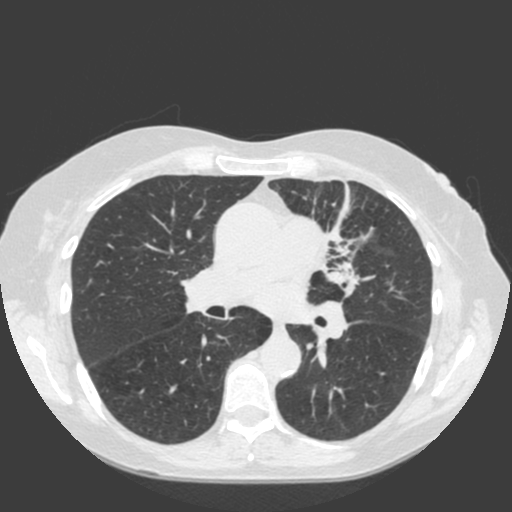
Low-dose screening chest CT, axial slice; baseline annual screen; lung window (W 1500 / L -600 HU); standard (soft-tissue) reconstruction kernel (C); slice 77 of 184 in the series. Female, age 66 years at enrolment. Current smoker at enrolment.
Expert reader's lesion annotation, bounding box [x1, y1, x2, y2] px = [275, 196, 403, 312]. The exam's reader record, not a measurement of the box and not confirmed to be the same lesion: non-calcified nodule or mass ≥4 mm, left upper lobe, 61 × 45 mm, spiculated (stellate) margins, soft tissue attenuation. Official screen result: positive, change unspecified: nodule(s) >= 4 mm or enlarging nodule(s), mass(es), or other non-specific abnormalities suspicious for lung cancer. Later outcome: lung cancer diagnosed 19 days after this screen — squamous cell carcinoma, keratinizing, NOS, left upper lobe, left hilum, mediastinum, left main stem bronchus, other location, poorly differentiated (G3), stage IIIB (AJCC 6th edition), 60 mm at pathology.